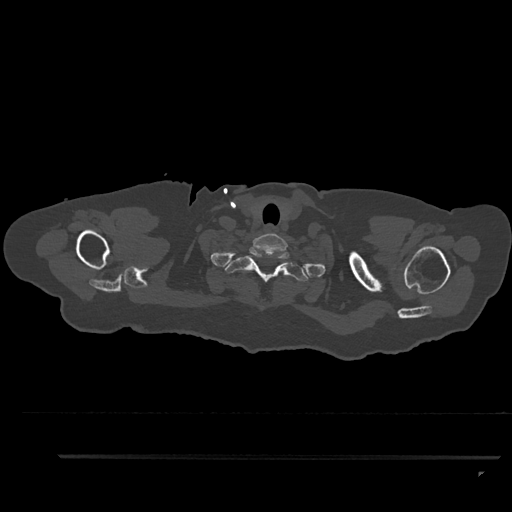
CT including the spine, one axial slice. Slice 772 of 797 in the series (ordered by position). Reconstruction kernel Br40s/3. 120 kVp. Bone window (W 1800 / L 400 HU). 0.5 mm slice thickness. 512 × 512 image matrix. Patient: female, 44 years. From the clinical record (not read from this slice): primary cancer: renal.
Annotated regions visible in this slice (semi-automatic segmentation, software-assisted and operator-edited):
- T1 vertebra: bounding box <225,246,309,282> (left, top, right, bottom; pixels)